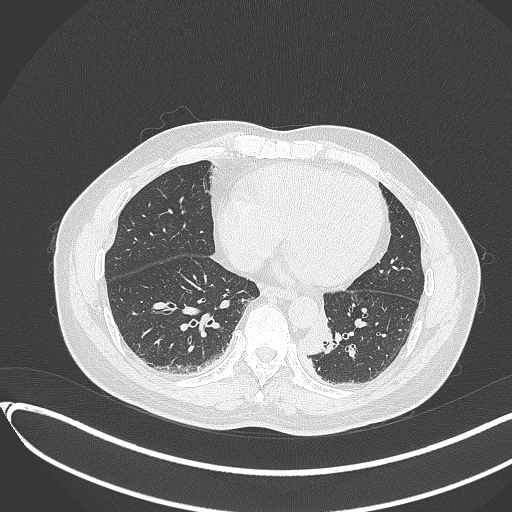
Chest CT, one axial slice. Position 111 of 417 along the scan axis. 120 kVp. Lung window (W 1500 / L -600 HU). 512 × 512 image matrix, field of view 400 × 400 mm. Male patient, age 54 years. From the clinical record (not read from this slice): clinical TNM (as recorded): T3 N0 M0.
Structures marked on this image (rectangle marked by the reading radiologist):
- lung tumour (recorded histology: squamous cell carcinoma): bounding box [x1, y1, x2, y2] px = [303, 306, 338, 356]